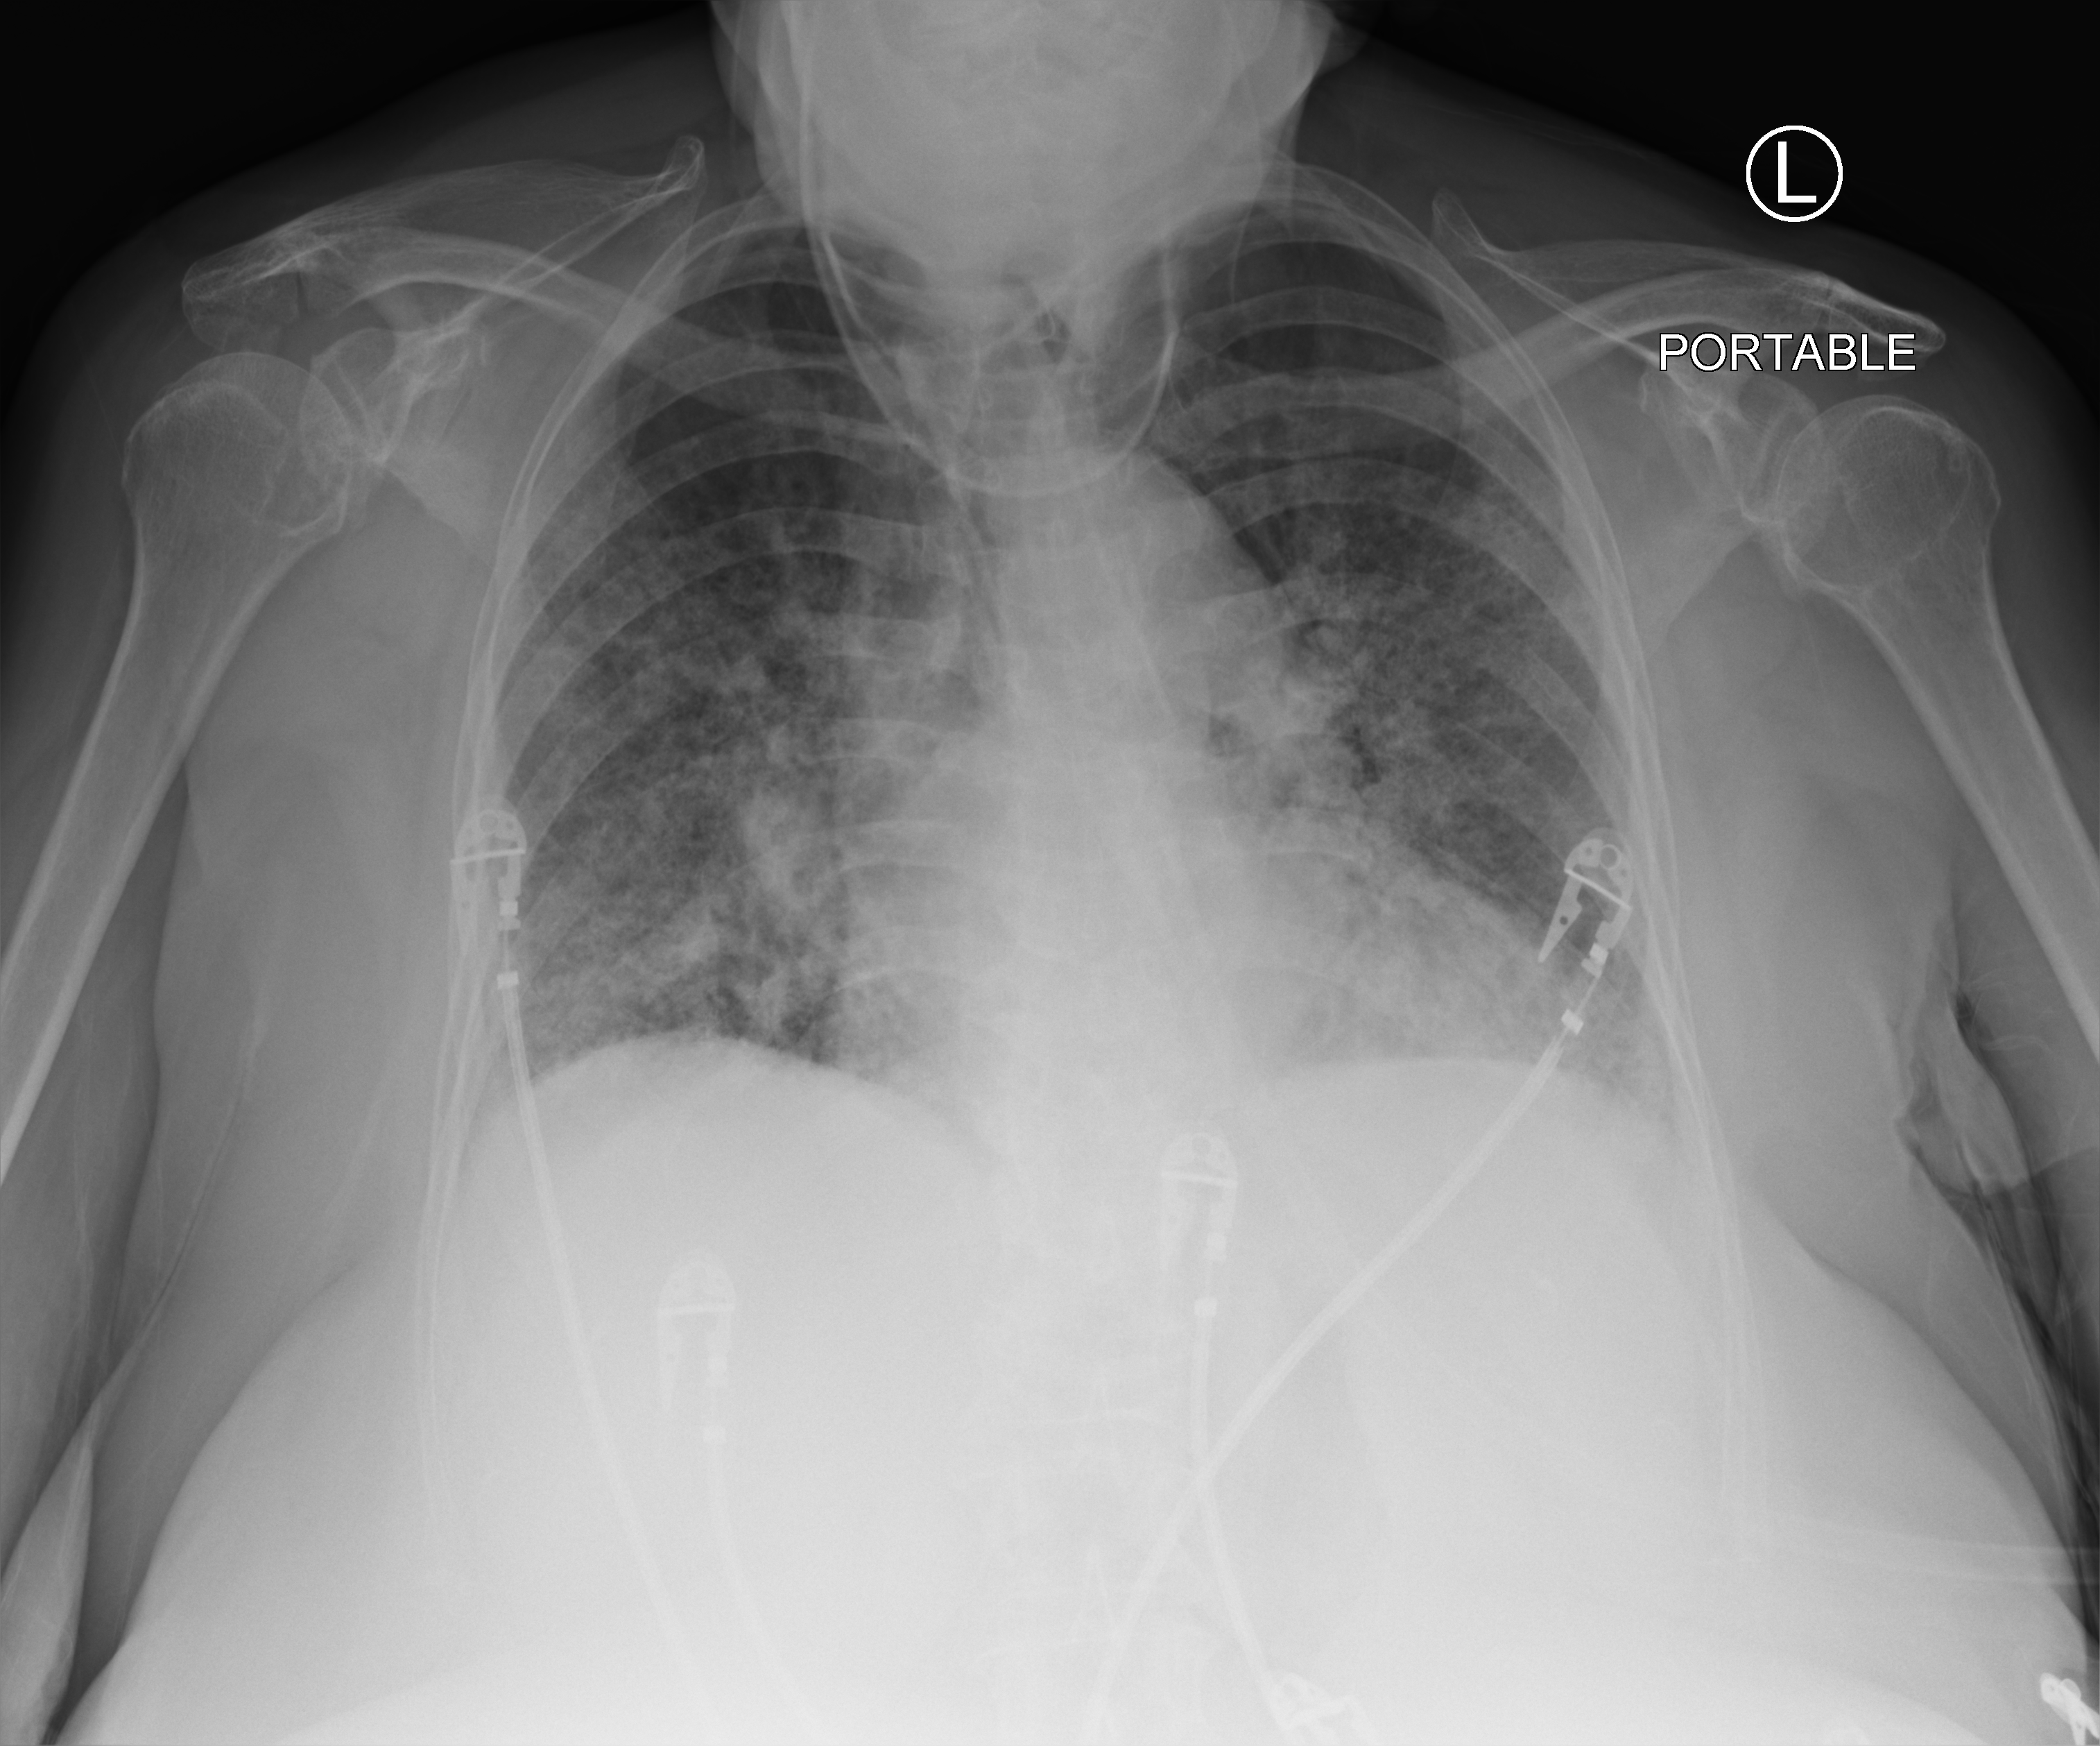
Chest X-ray (portable), anteroposterior (AP) projection. Female patient hospitalised with COVID-19, age 75–90 years.
Hospital-stay facts (about this admission, not read from this image; timing relative to this image not recorded): mechanically ventilated during this hospital stay: no; admitted to intensive care during this hospital stay: no.